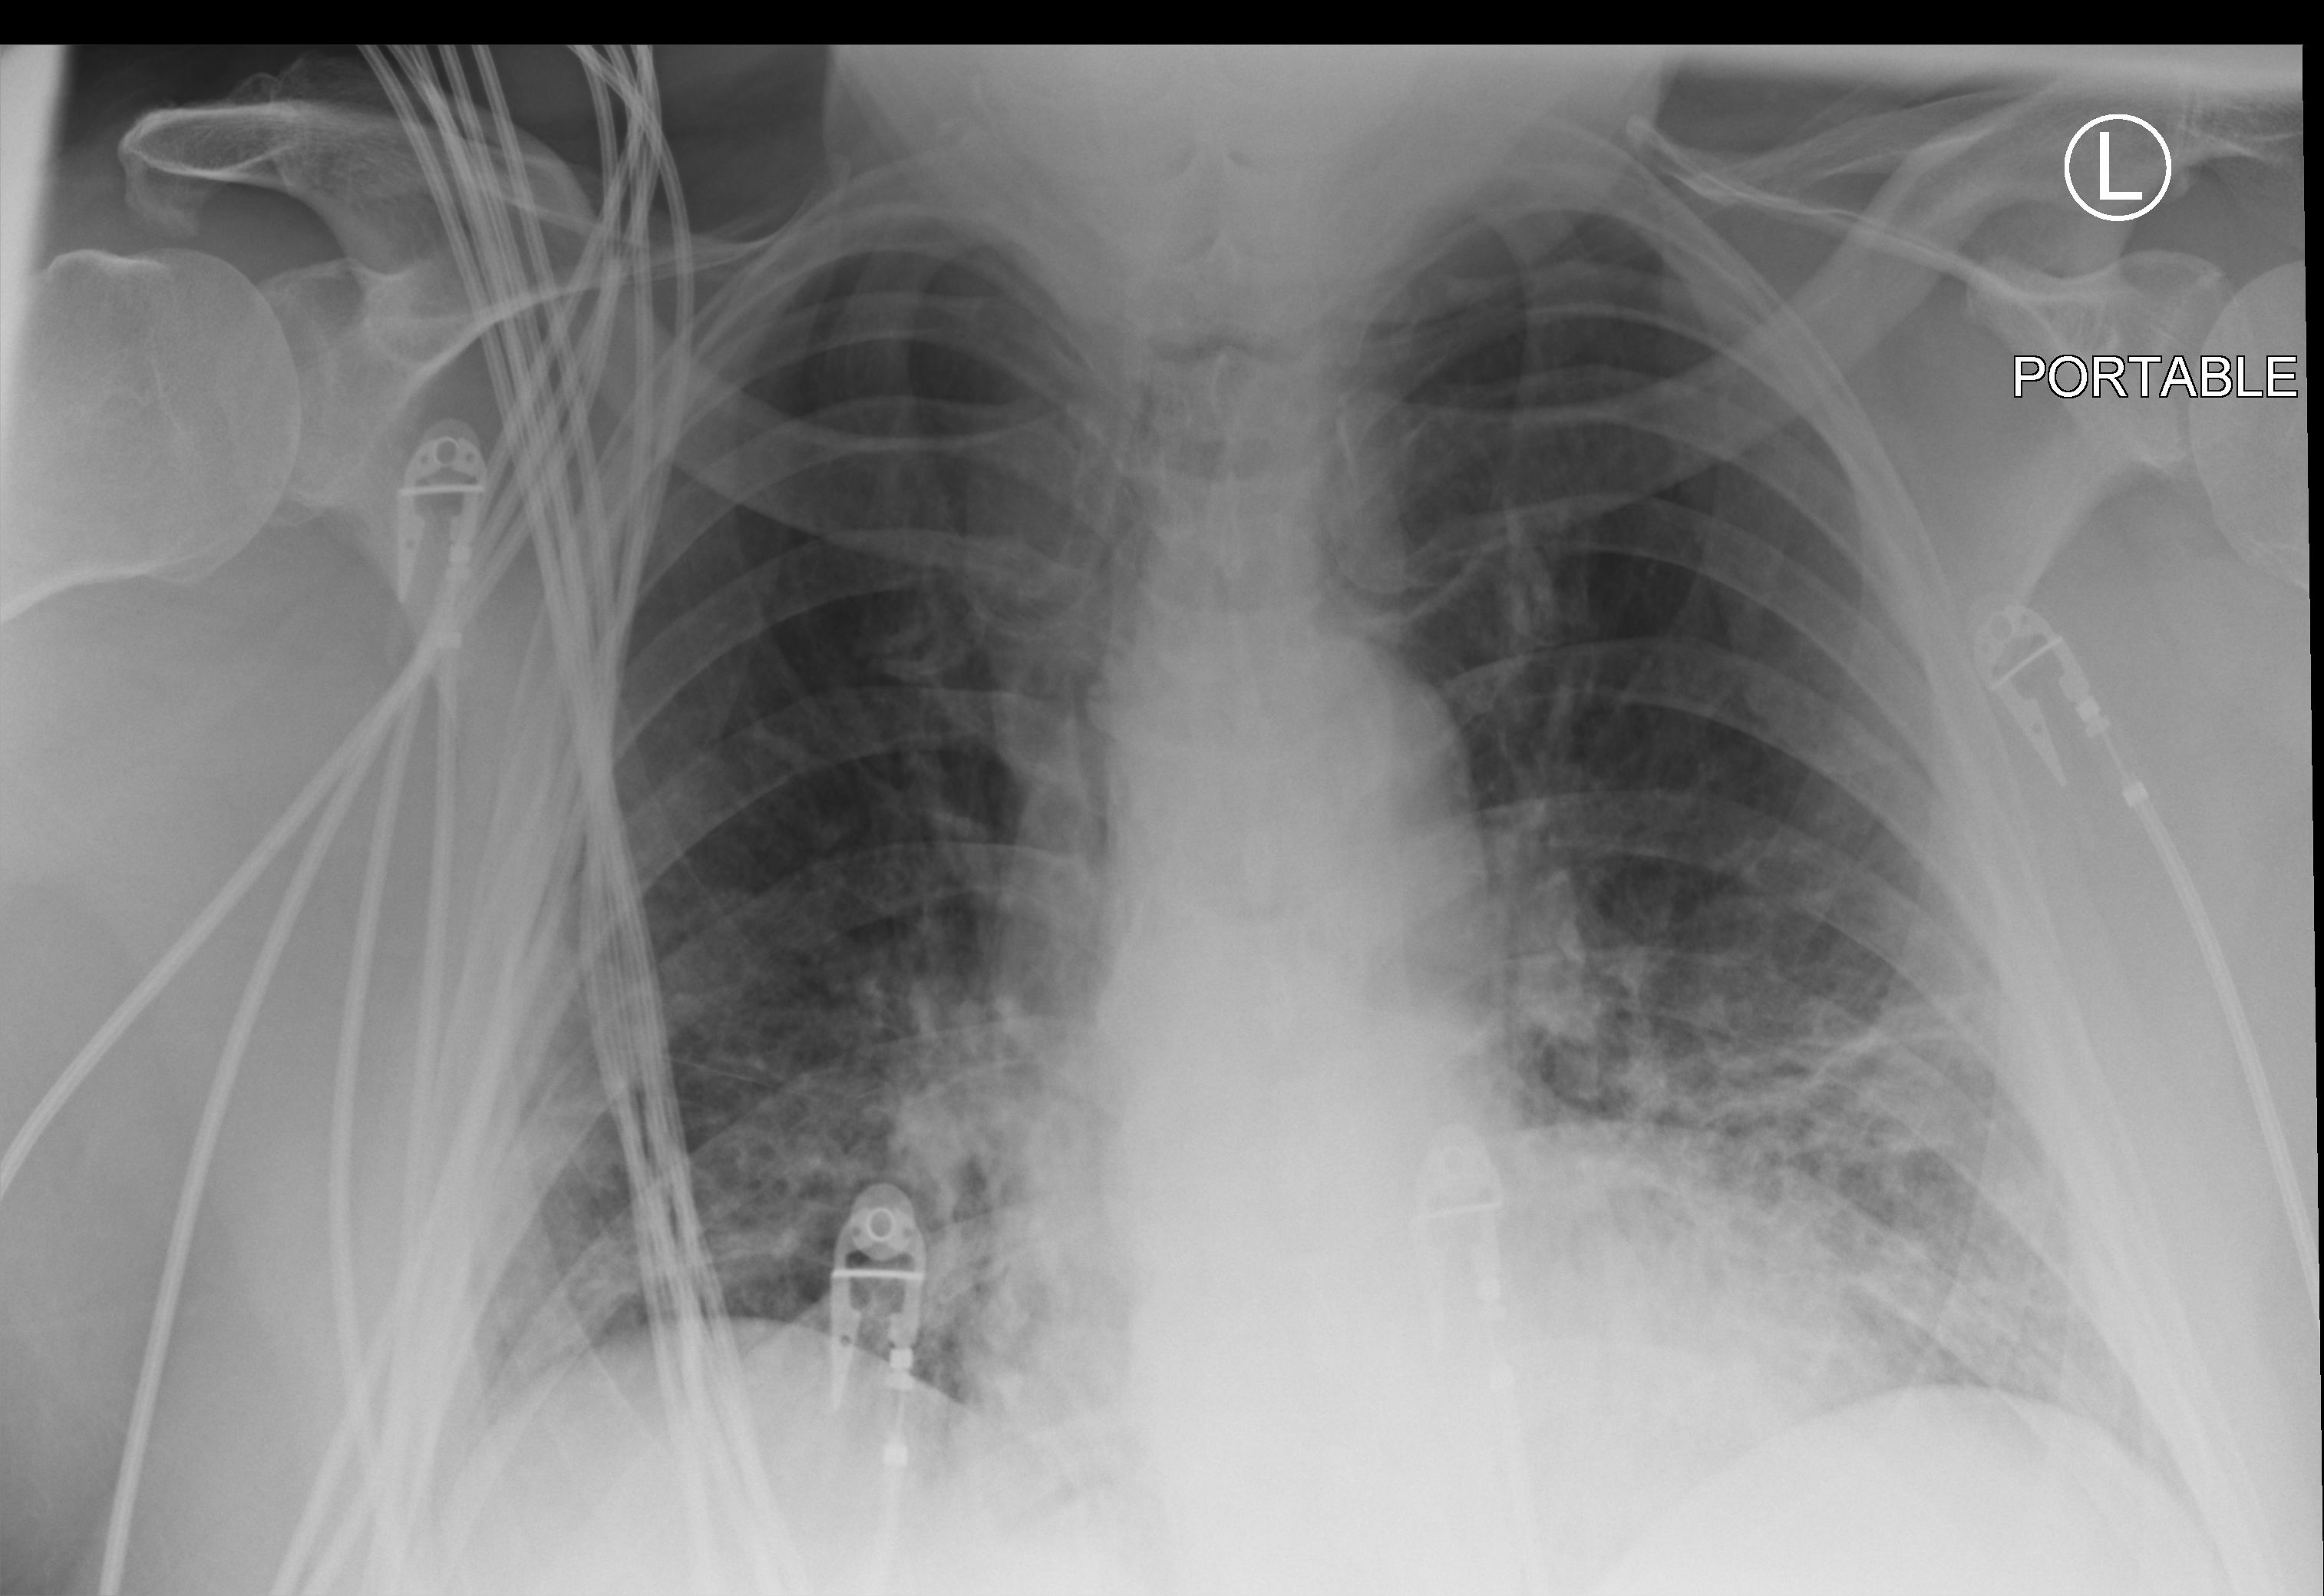
Chest X-ray (portable); anteroposterior (AP) projection. Male patient hospitalised with COVID-19, age 18–59 years.
Hospital-stay facts (about this admission, not read from this image; timing relative to this image not recorded):
- admitted to intensive care during this hospital stay: yes
- length of hospital stay: 21 days
- chronic kidney disease (admission record): no